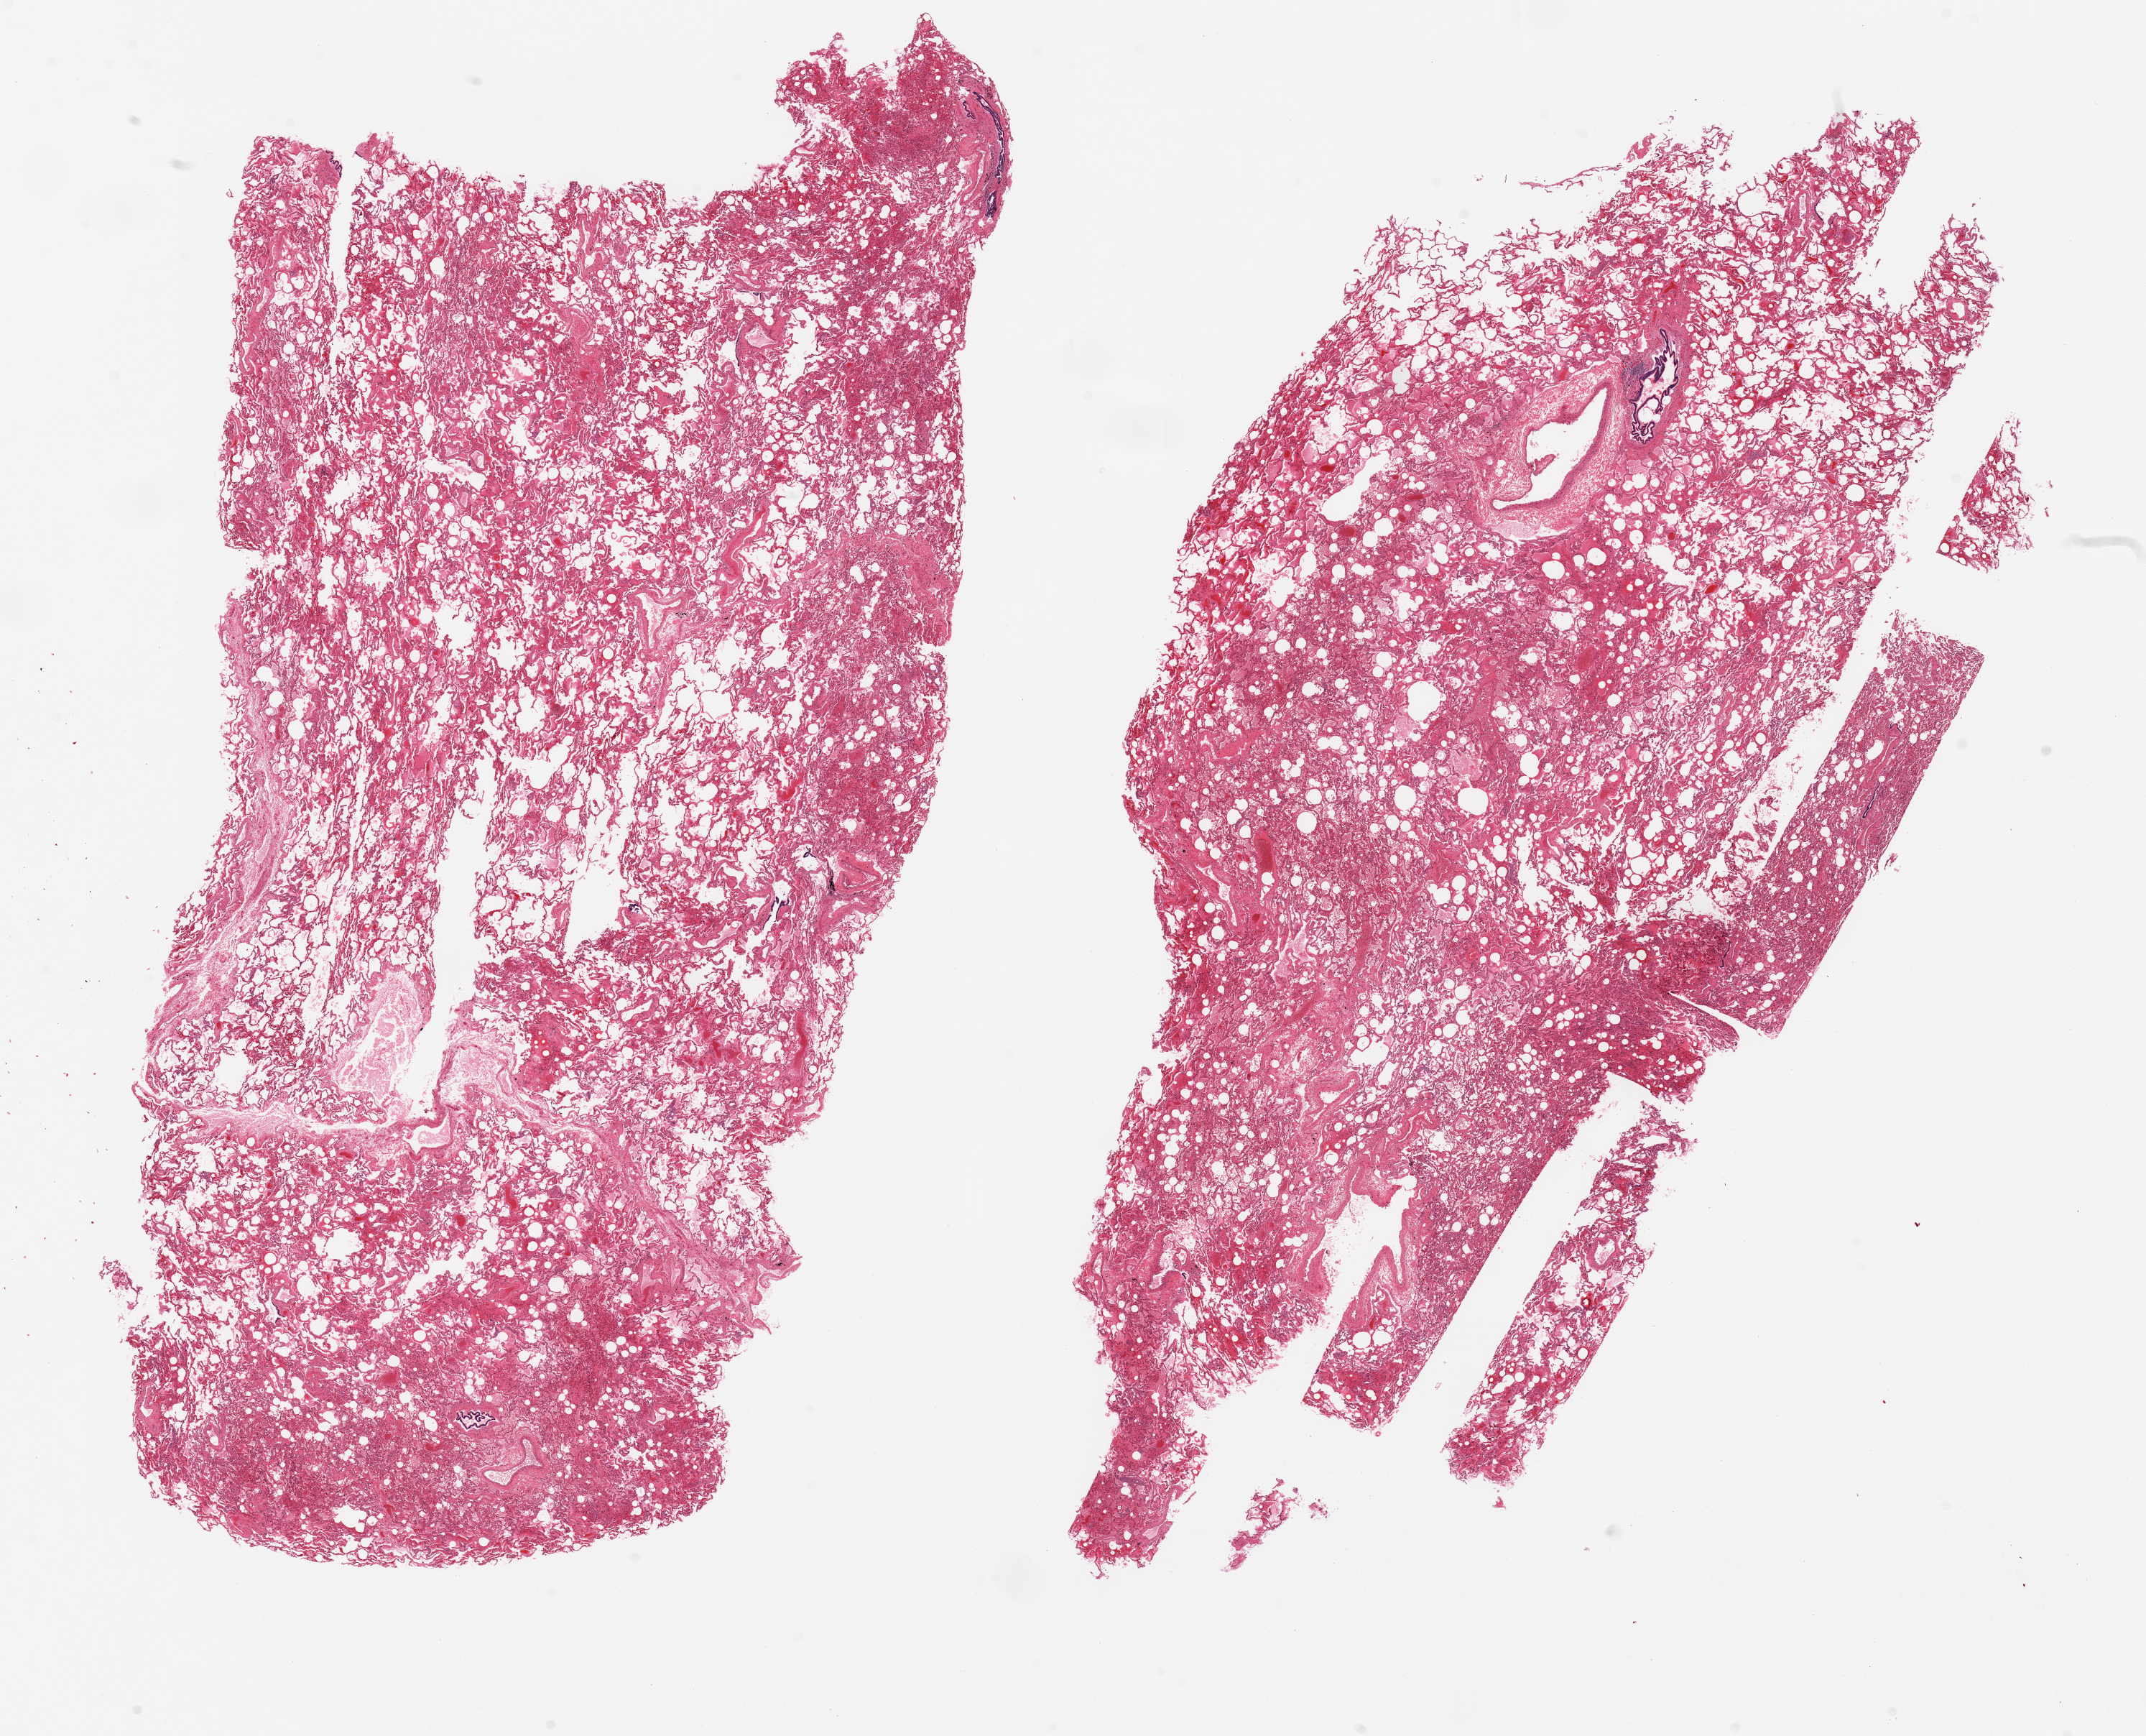
Hematoxylin and eosin (H&E) whole-slide image — low-resolution overview of the scanned area, about 23.6 x 19.1 mm (from a 20x scan); PAXgene-fixed paraffin-embedded (PFPE) section; sampled site (target tissue): lung; tissue donor sample.
Review note (as recorded): 2 pieces; patchy edema and hemorrhage.